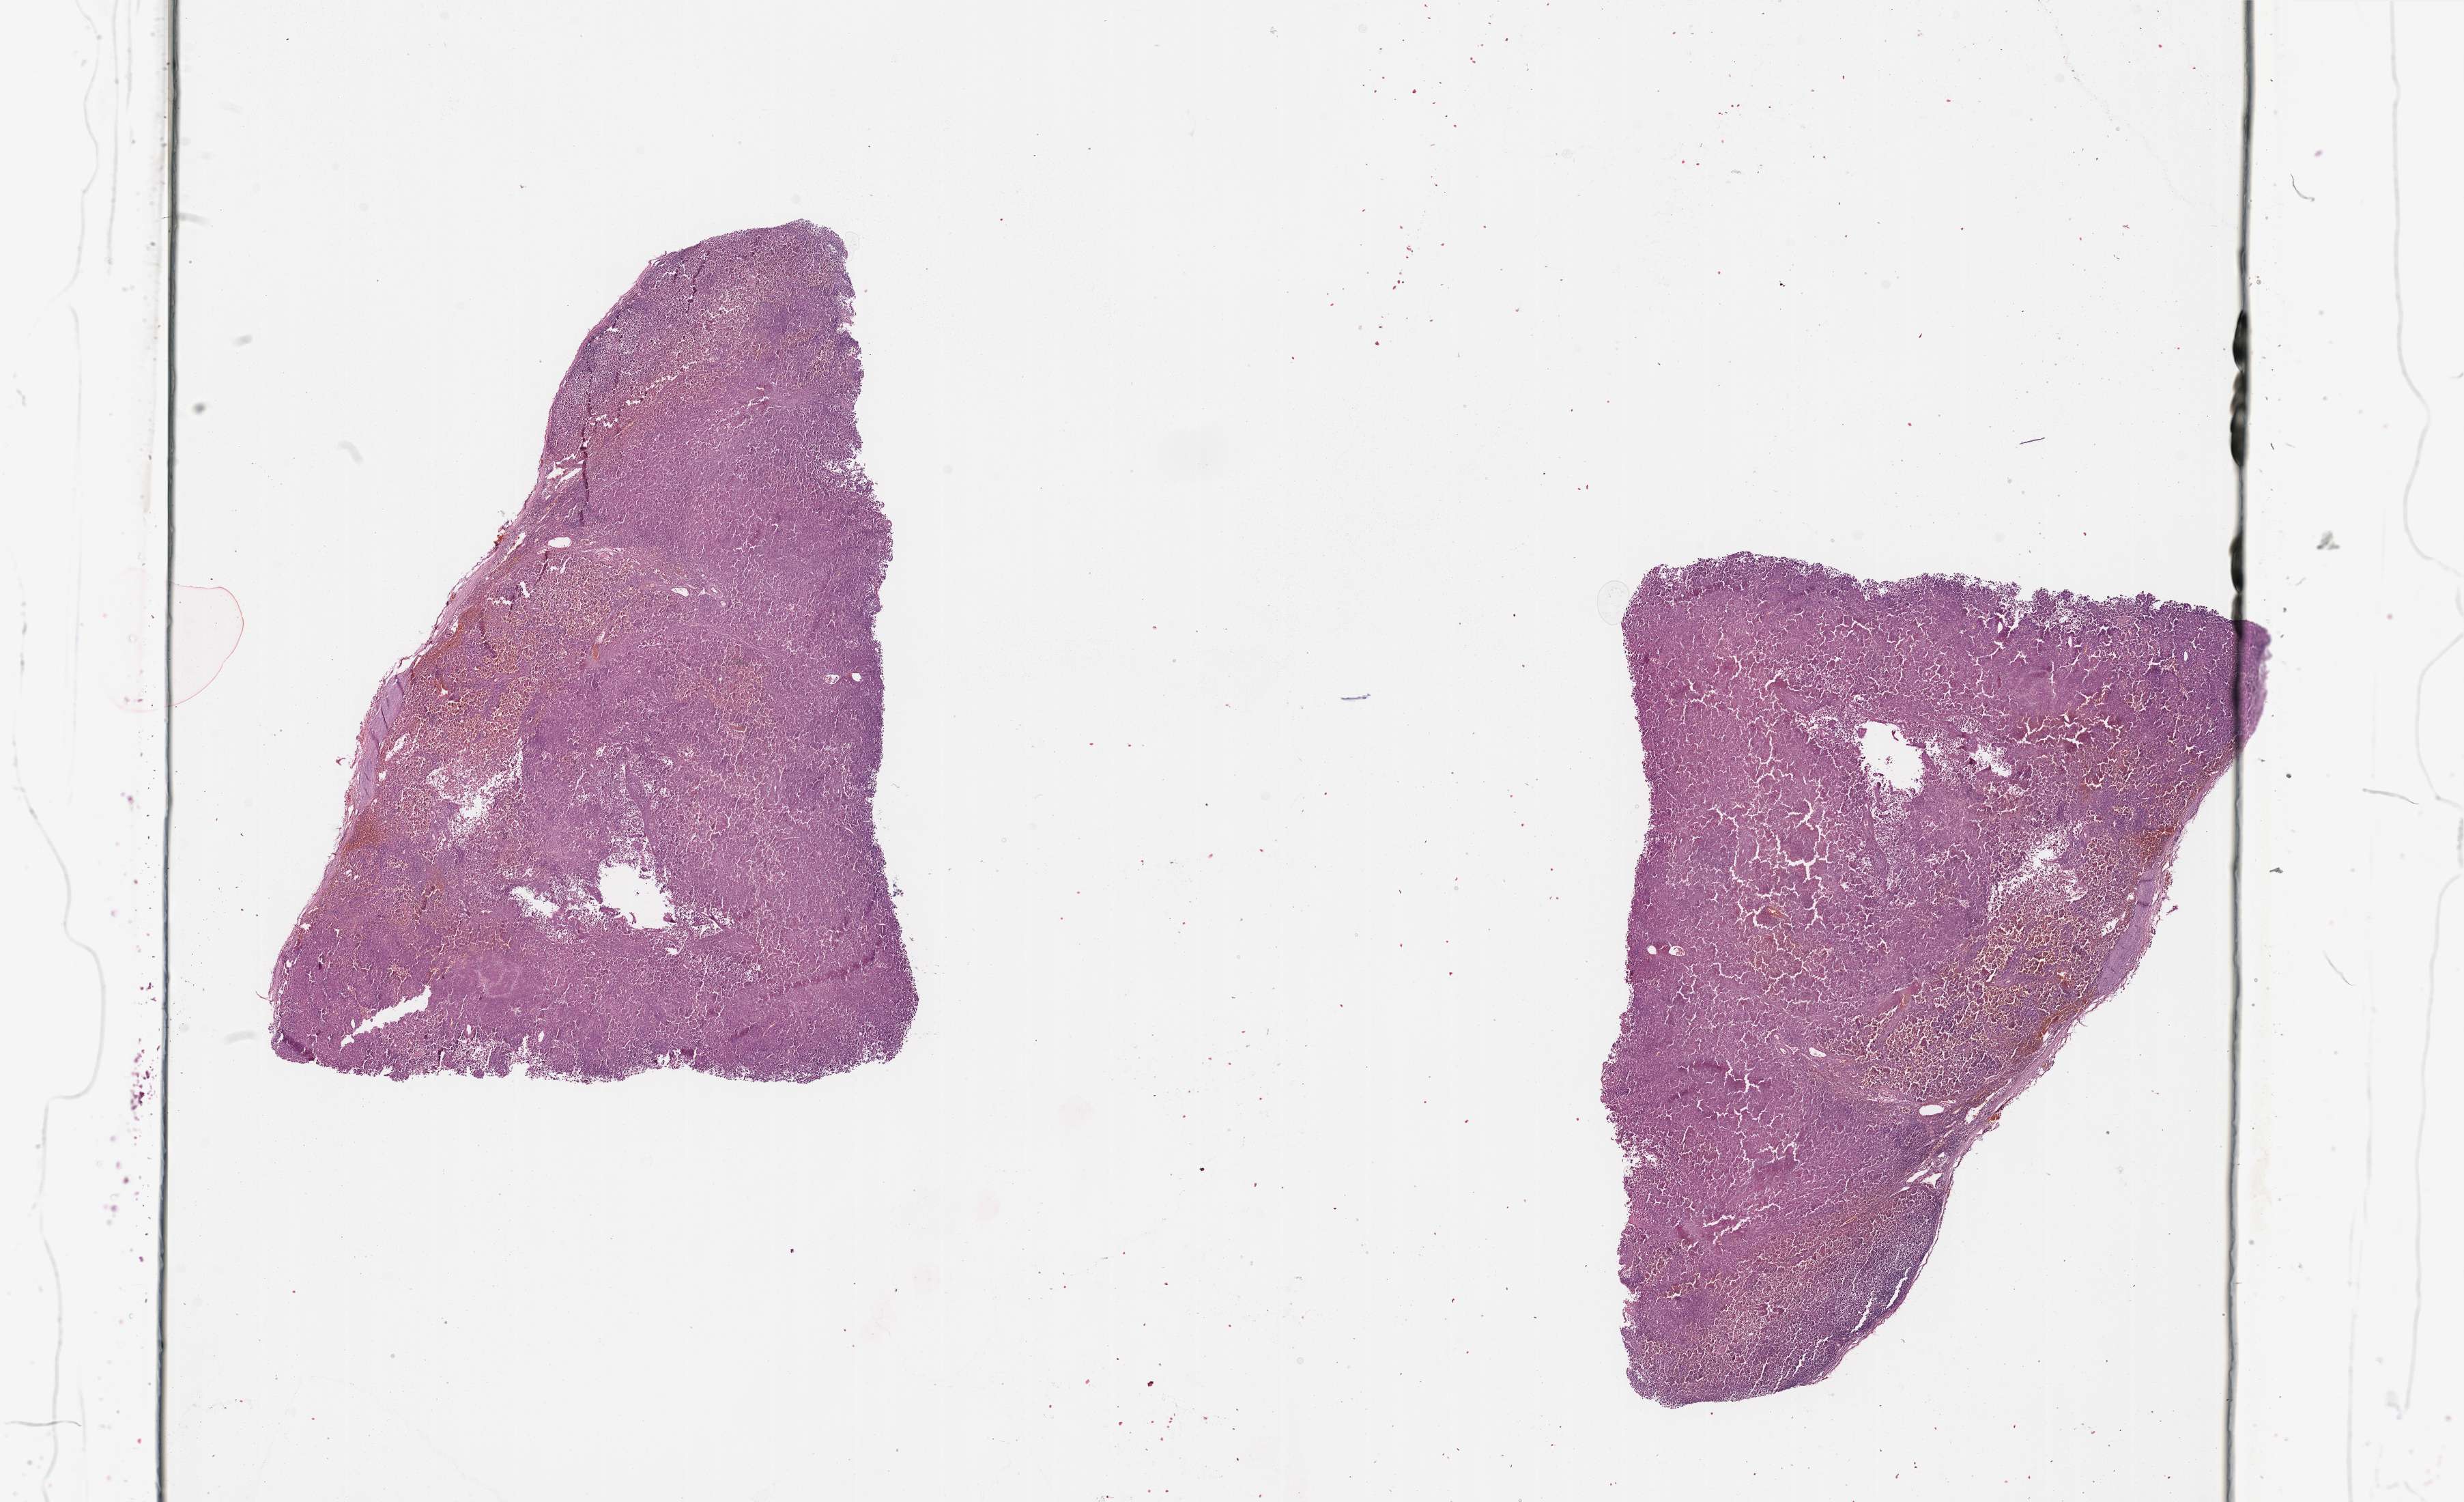
Whole-slide histology image, H&E-stained — a low-resolution overview of the entire scanned area, about 28.5 x 17.4 mm (from a 20x scan). Tumour tissue sample, sampled site: lymph node. 32-year-old male patient. Composition of this section per pathologist review: tumour nuclei 90%, necrosis 5%.
- this section: metastatic tumour tissue
- patient diagnosis: Malignant melanoma, NOS
- primary tumour site (as recorded): extremities